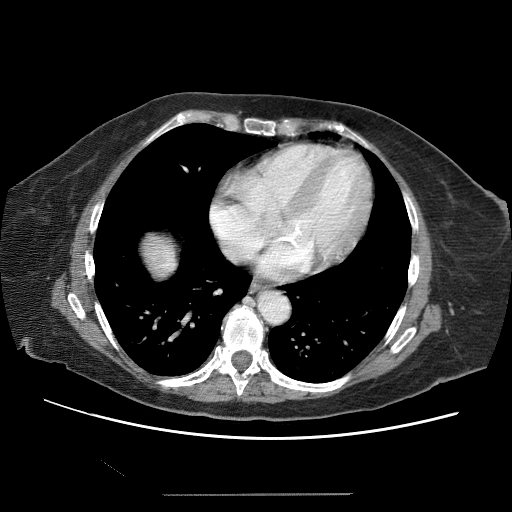
Contrast-enhanced abdominal CT (liver protocol), one axial slice; slice 63 of 65 in the series (ordered by position); soft-tissue window (W 400 / L 40 HU); 512 × 512 image matrix. From the clinical record (not read from this slice): diagnosis: hepatocellular carcinoma (patient treated with transarterial chemoembolisation; whether this scan precedes or follows treatment is not stated here); TNM stage (as recorded): Stage-IIIB; Child-Pugh class: A; tumour nodularity: uninodular.
Outlined on this slice (semi-automatic segmentation, software-assisted and operator-edited):
- abdominal aorta: bounding box [x1, y1, x2, y2] px = [260, 292, 290, 324]
- liver parenchyma outside the tumour (the mass and vessels are separate outlines, so this box may not span the whole liver): [154, 250, 164, 262]